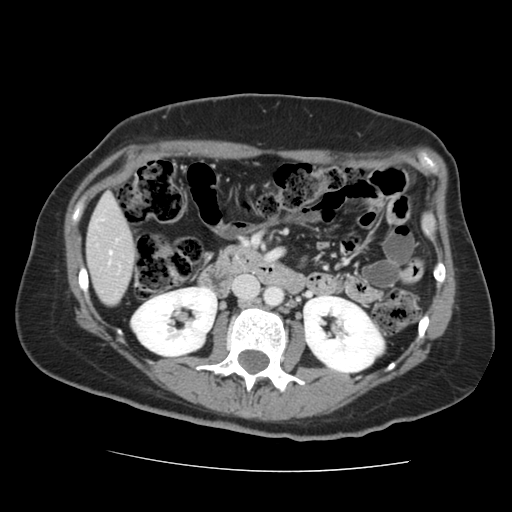
Contrast-enhanced abdominal CT, one axial slice. Position 54 of 144 along the scan axis. 120 kVp. Intravenous contrast given. Soft-tissue window (W 400 / L 40 HU). 2.5 mm slice thickness. 512 × 512 image matrix, field of view 333 × 333 mm. Female patient, age 46 years. From the clinical record (not read from this slice): diagnosis: colorectal cancer liver metastases, imaged before liver resection.
Structures marked on this image (expert manual segmentation):
- liver: bounding box (x1, y1, x2, y2) in pixels: (88, 197, 133, 304)
- planned liver remnant (the part of the liver to remain after resection): (88, 197, 133, 276)
- portal vein (with intrahepatic branches): (109, 252, 111, 255)